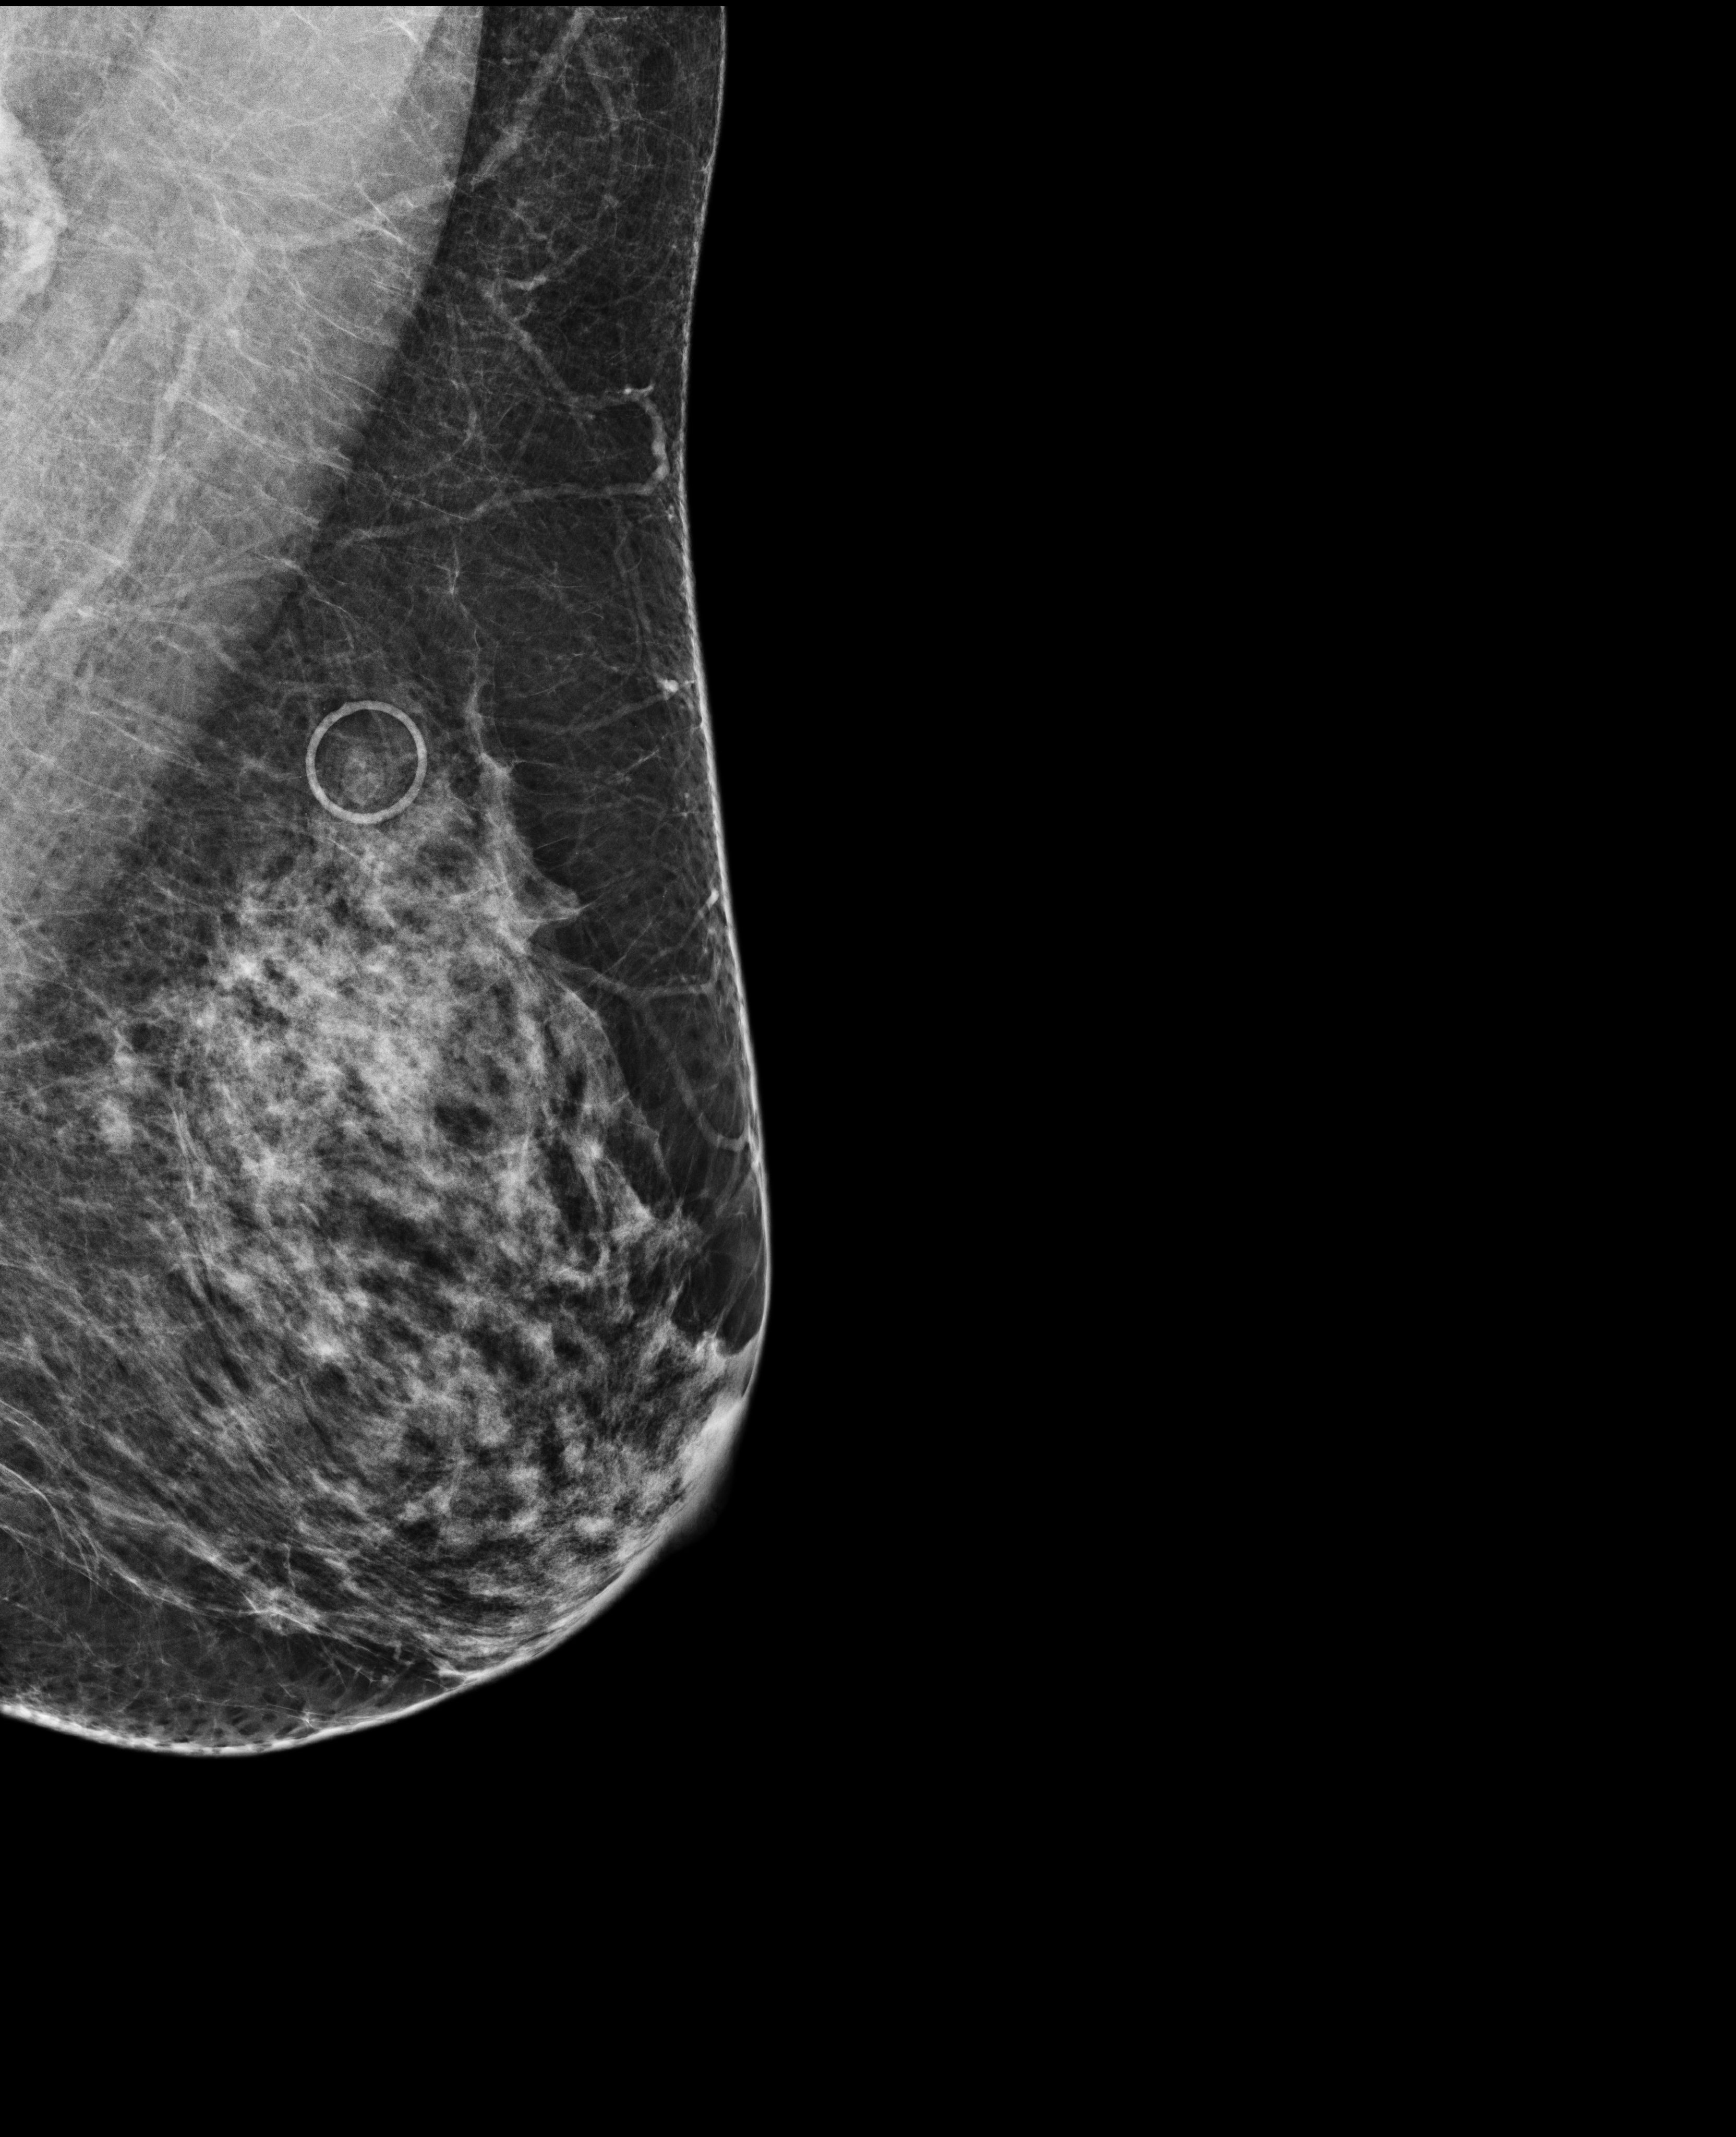
Full-field digital mammogram (FFDM); left breast; medio-lateral oblique projection; screening examination. Patient: female, 52 years.
Breast density at the screening exam (both breasts): heterogeneously dense (BI-RADS density category c). Final BI-RADS assessment for this screening round (tomosynthesis exam, both breasts): category 1. Recall: no recall after this screen.